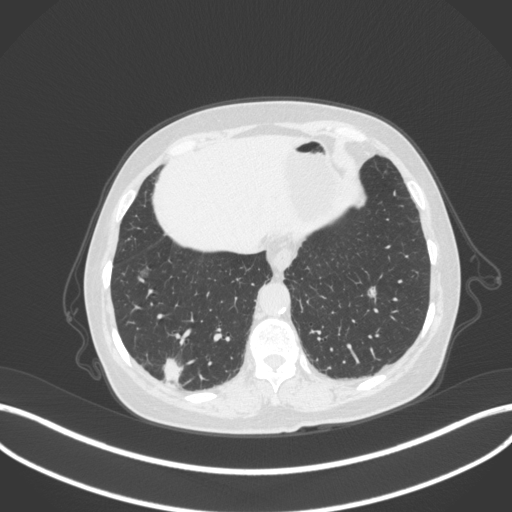
Chest CT, one axial slice; position 64 of 340 along the scan axis; reconstruction kernel B31f; lung window (W 1500 / L -600 HU); 512 × 512 image matrix, field of view 400 × 400 mm. Female patient, age 69 years. Case-level facts recorded for this patient, not image findings: clinical TNM (as recorded): T1b N0 M0.
Outlined on this slice (bounding box drawn by a radiologist):
- lung tumour (recorded histology: adenocarcinoma): box from (x=161, y=354) to (x=185, y=387) px